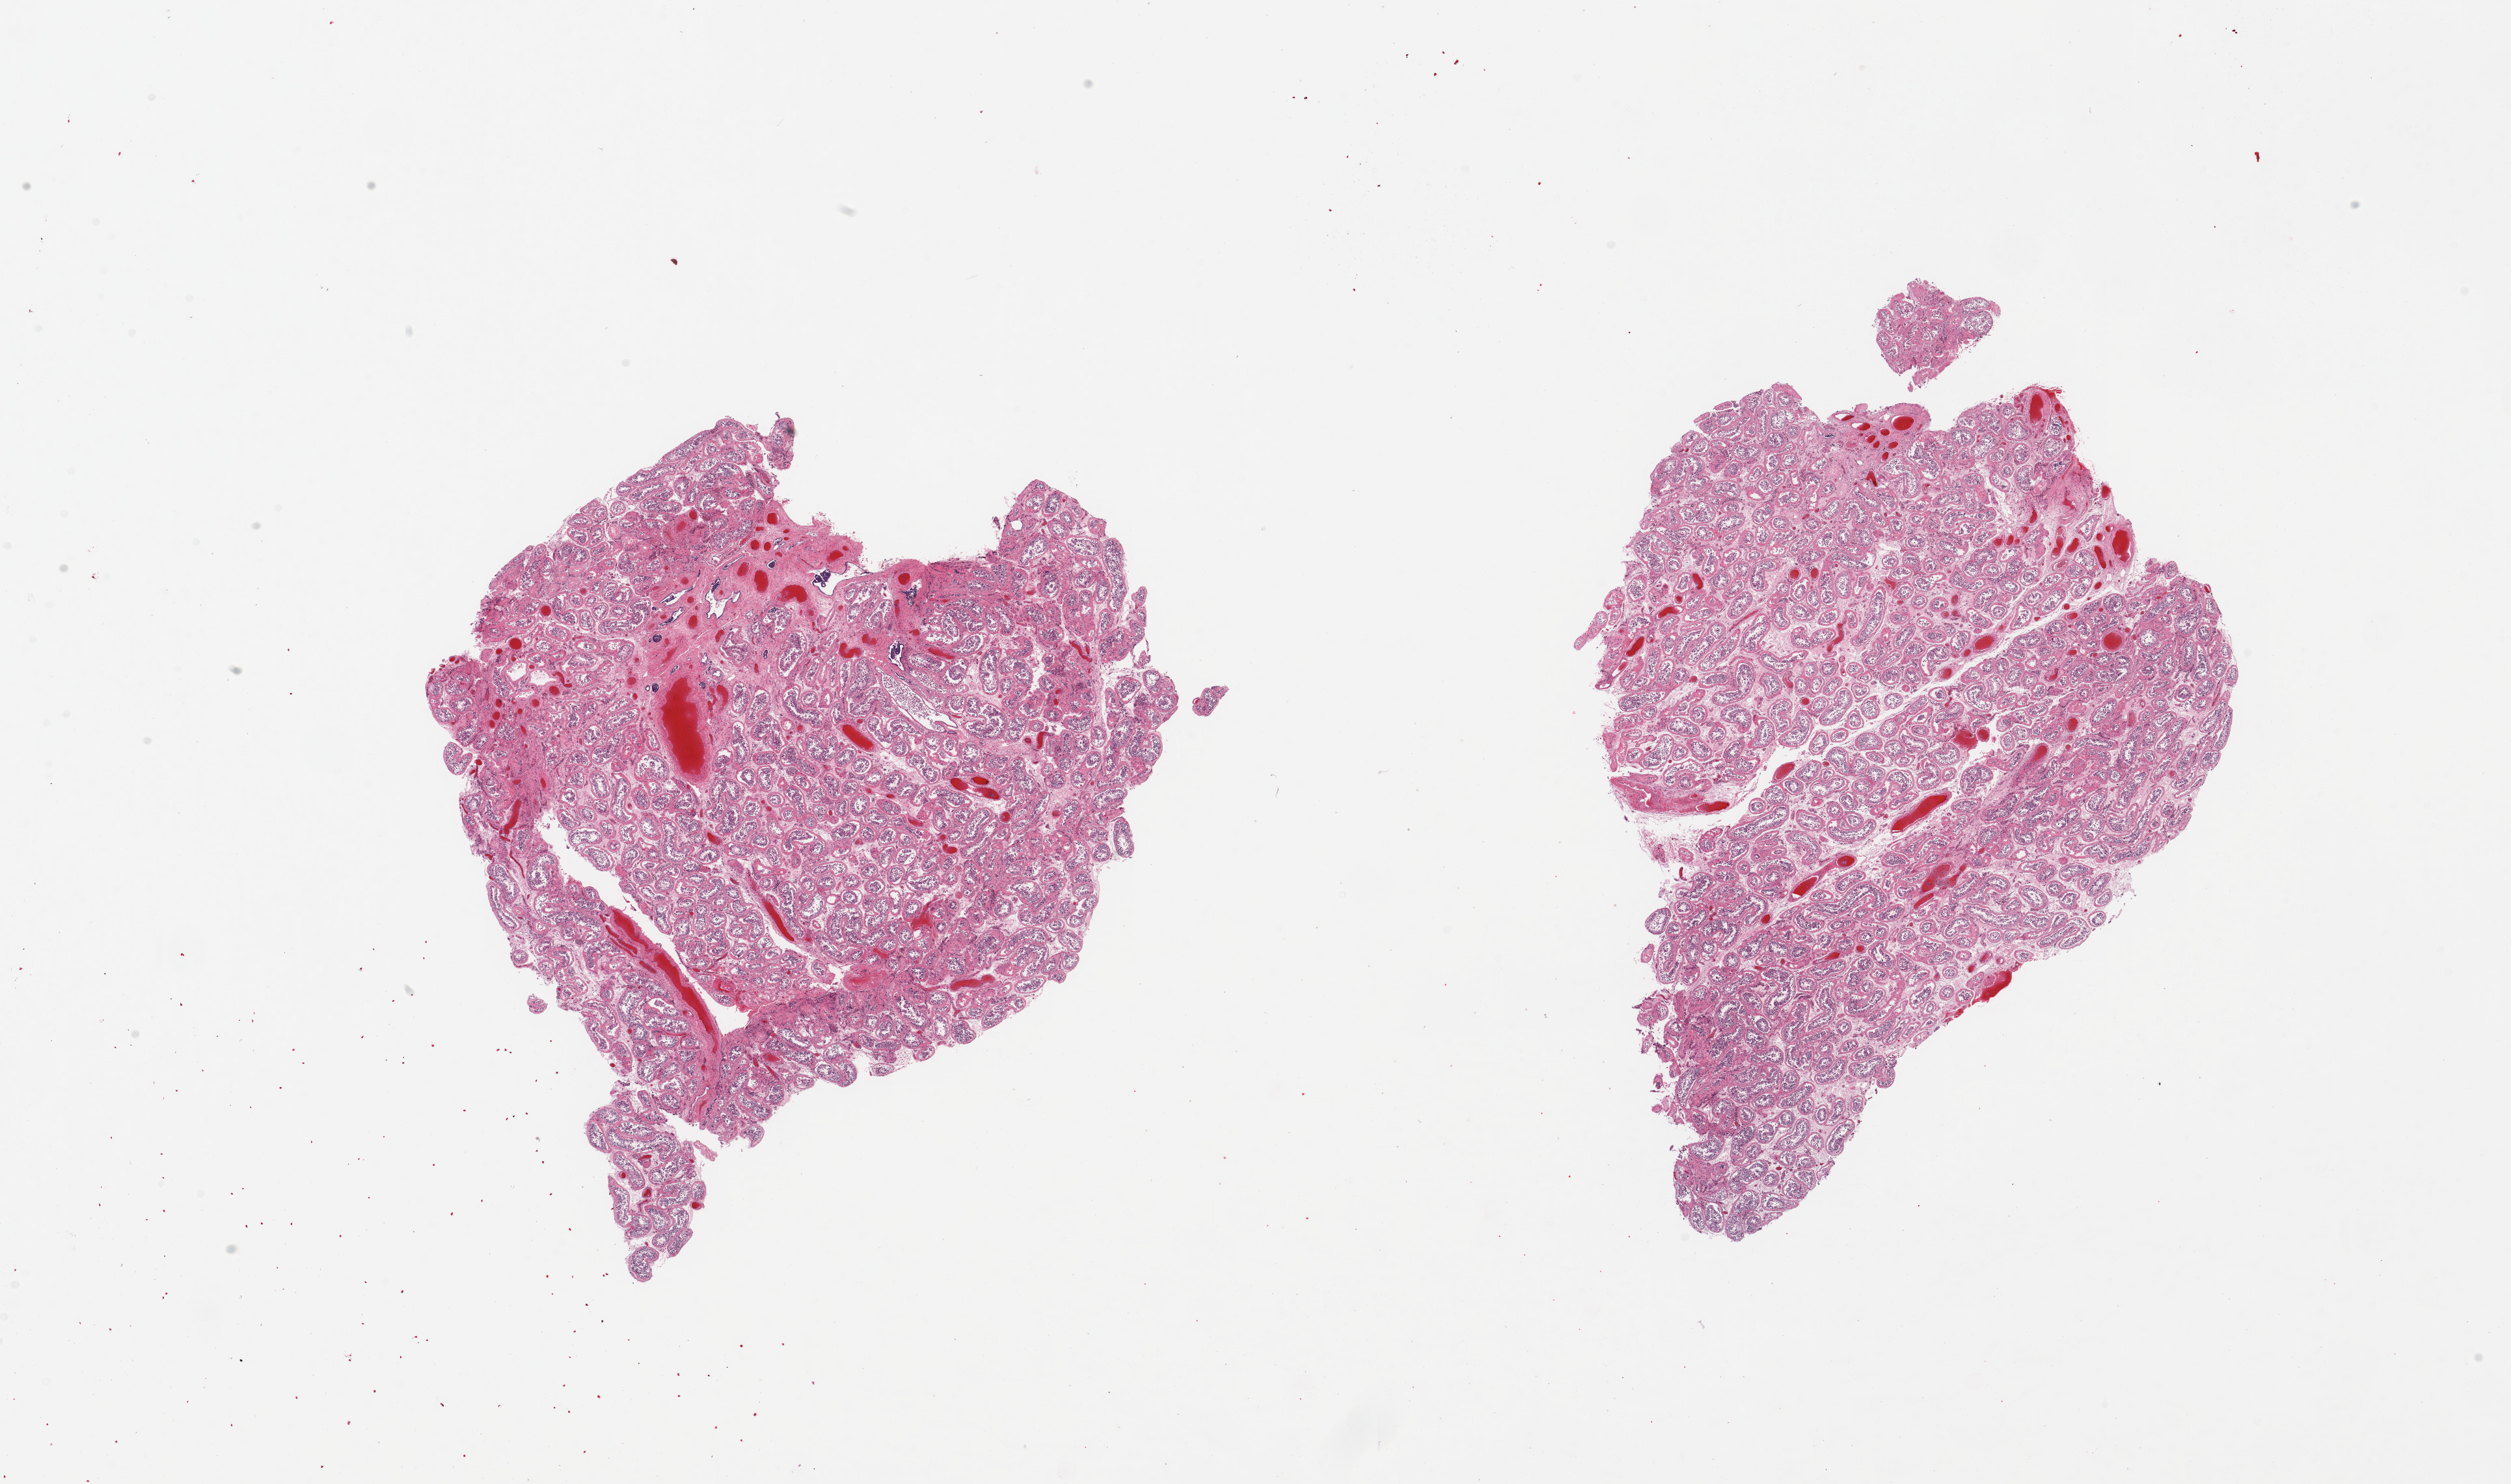
Whole-slide image, H&E stain — low-resolution overview of the scanned area, about 30.5 x 18.0 mm, PAXgene-fixed, paraffin-embedded tissue, sampled site (target tissue): testis, donor tissue sample. Donor sex: male.
• pathologist's review note for this sample: 2 pieces; 1 contains focus of rete testis <10% area